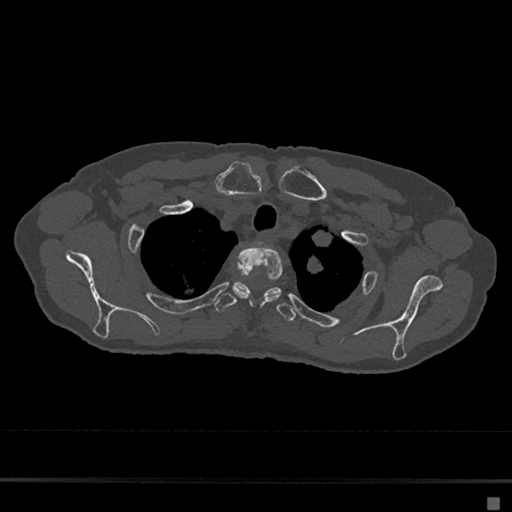
CT including the spine, one axial slice. Position 563 of 797 along the scan axis. Reconstruction kernel Br40s/3. 120 kVp. Bone window (W 1800 / L 400 HU). 0.5 mm slice thickness. 512 × 512 image matrix, field of view 360 × 360 mm. Patient: female, 68 years. From the clinical record (not read from this slice): primary cancer: renal.
Outlined on this slice (semi-automatically segmented with operator editing):
- T1 vertebra: bounding box <257,243,260,246> (left, top, right, bottom; pixels)
- T2 vertebra: <233,246,283,303>
- T3 vertebra: <214,282,297,322>